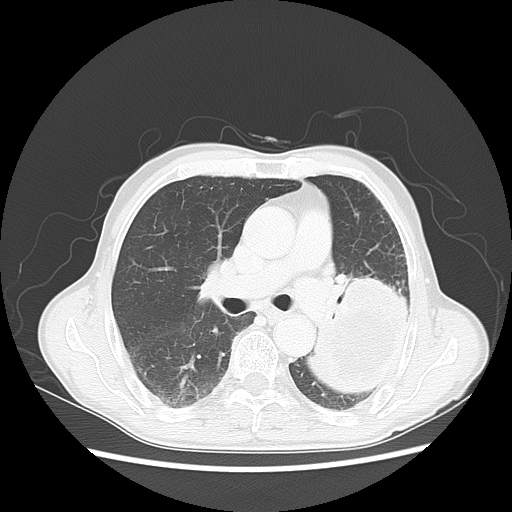
Chest CT, one axial slice; slice 31 of 51 in the series (ordered by position); 120 kVp; lung window (W 1500 / L -600 HU); 5 mm slice thickness; 512 × 512 image matrix. Patient: male, 64 years. Case-level facts recorded for this patient, not image findings: clinical TNM (as recorded): T4 N0 M0; histopathological grade: G2-3.
Outlined on this slice (bounding box drawn by a radiologist):
- lung tumour (recorded histology: squamous cell carcinoma): bounding box [x1, y1, x2, y2] px = [306, 274, 416, 396]